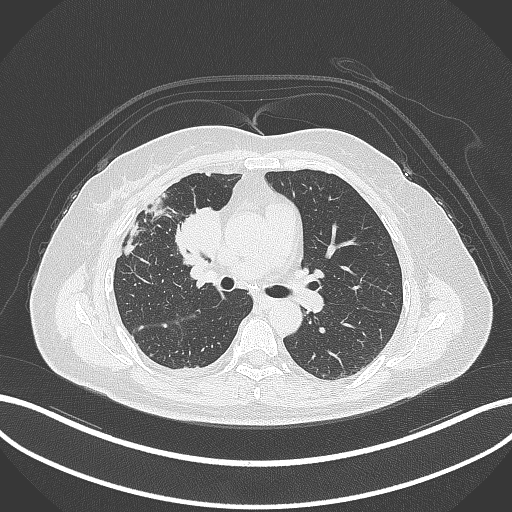
Chest CT, one axial slice. Slice 163 of 305 in the series (ordered by position). Lung window (W 1500 / L -600 HU). 512 × 512 image matrix, field of view 400 × 400 mm. Female patient, age 52 years. From the clinical record (not read from this slice): clinical TNM (as recorded): T3 N1 M1.
Annotated regions visible in this slice (bounding box drawn by a radiologist):
- lung tumour (recorded histology: adenocarcinoma): bounding box (x1, y1, x2, y2) in pixels: (175, 206, 226, 262)